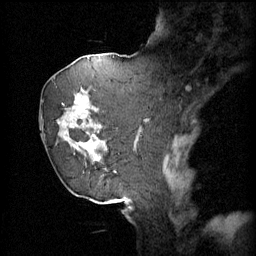
Breast MRI (dynamic contrast-enhanced), one sagittal slice; 4 images stored at this slice position (order not interpretable as contrast timing); 1.5 T; TE 4.2 ms, TR 11 ms; 2 mm slice thickness; 256 × 256 image matrix, field of view 220 × 220 mm. Female patient, age 72 years.
Annotated regions visible in this slice (semi-automatically segmented with operator editing):
- analysis volume of interest (the breast-tissue region the enhancement analysis was run in; not a lesion): bounding box (x1, y1, x2, y2) in pixels: (47, 68, 109, 163)
- tumour enhancement mask (voxels above the 70 % enhancement threshold inside the analysis volume of interest): (64, 88, 109, 147)